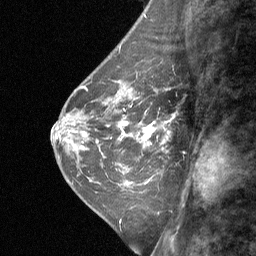
Breast MRI (dynamic contrast-enhanced), one sagittal slice. Slice 23 of 64 in the series (ordered by position). Dynamic contrast-enhanced study with each time point stored as its own series, time point 2 of 3 at this slice position (early post-contrast, ordered by acquisition time). 1.5 T. TE 4.8 ms, TR 27 ms. 2 mm slice thickness. 256 × 256 image matrix, field of view 180 × 180 mm. Patient: female, 42 years. Case-level facts recorded for this patient, not image findings: setting: breast cancer imaged before/during neoadjuvant chemotherapy; receptor status: triple-negative.
Structures marked on this image (semi-automatic segmentation, software-assisted and operator-edited):
- analysis volume of interest (the breast-tissue region the enhancement analysis was run in; not a lesion): box from (x=124, y=94) to (x=174, y=161) px
- tumour enhancement mask (voxels above the 90 % enhancement threshold inside the analysis volume of interest): (x=142, y=122)–(x=168, y=143)